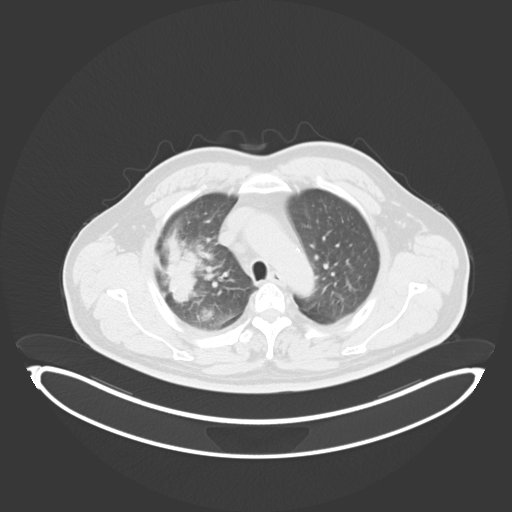
Chest CT, one axial slice. Slice 225 of 284 in the series (ordered by position). Reconstruction kernel B30f. Lung window (W 1500 / L -600 HU). 3 mm slice thickness. 512 × 512 image matrix, field of view 500 × 500 mm. Male patient, age 55 years. From the clinical record (not read from this slice): clinical TNM (as recorded): T3 N2 M1.
Structures marked on this image (rectangle marked by the reading radiologist):
- lung tumour (recorded histology: adenocarcinoma): bounding box [x1, y1, x2, y2] px = [163, 226, 203, 309]